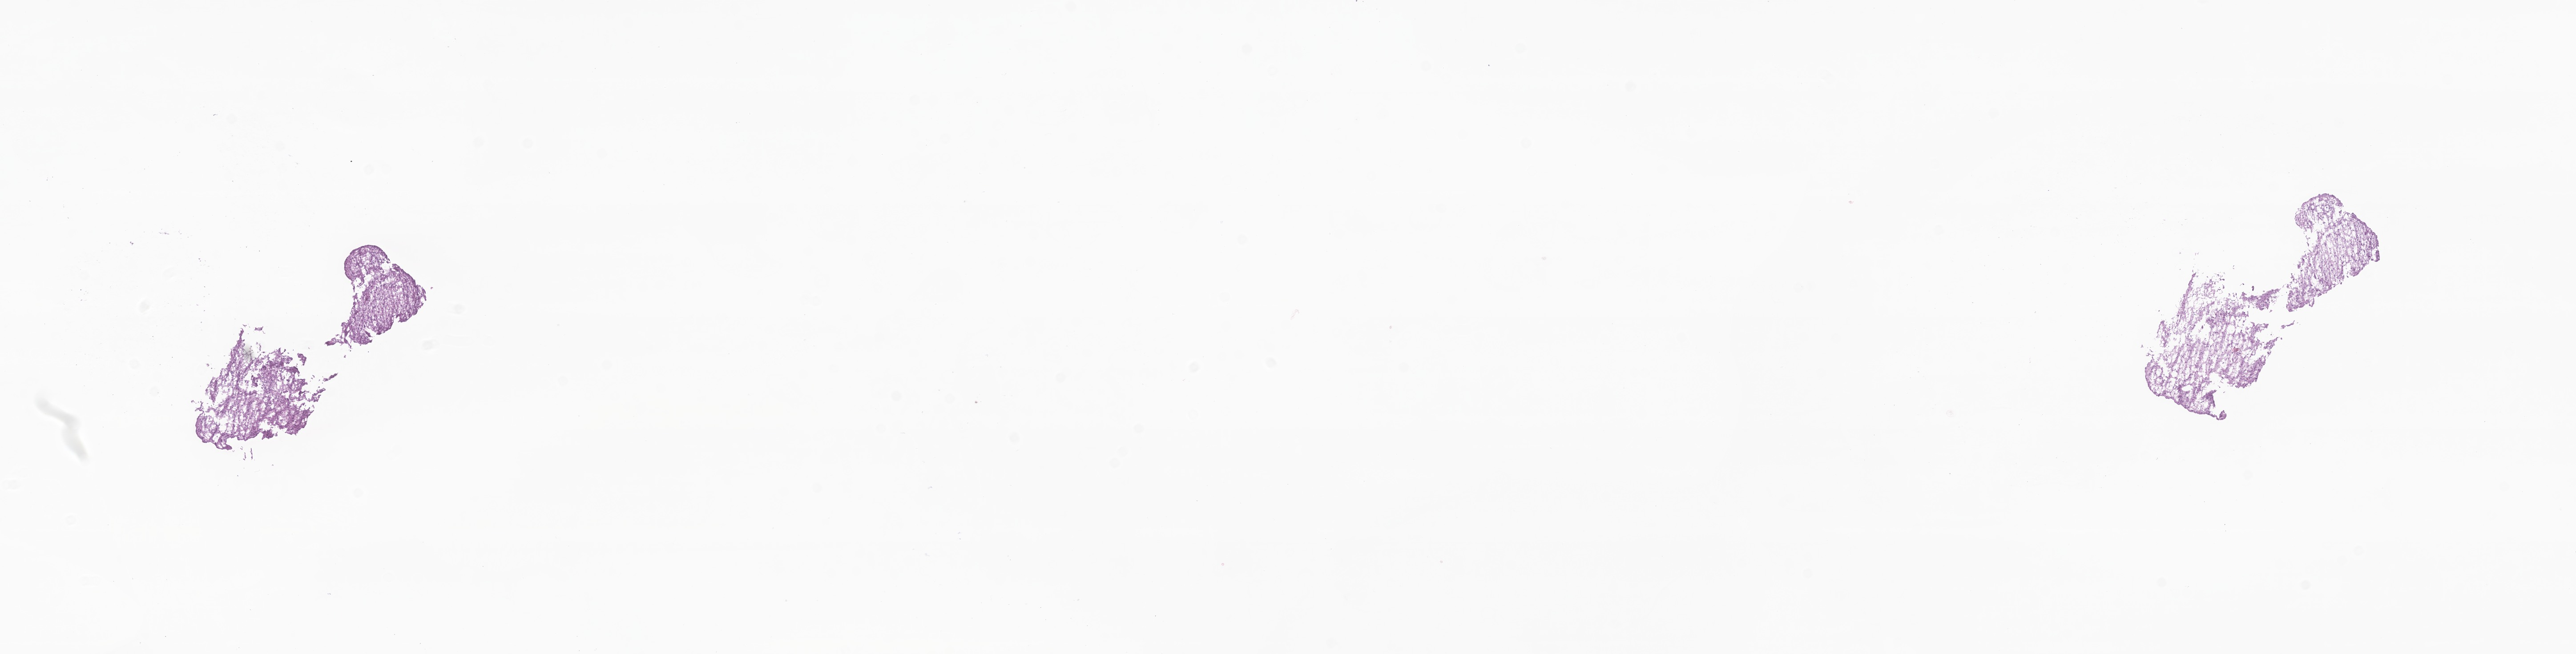
Digitized H&E-stained section of tumor tissue from the optic nerve, whole scanned area (about 24.4 x 6.2 mm) shown as a low-resolution overview, cryosection (OCT / tissue freezing medium). Female patient, age 212 months (17 years 8 months).
Diagnosis (ICD-O-3 morphology term): Pilocytic astrocytoma.